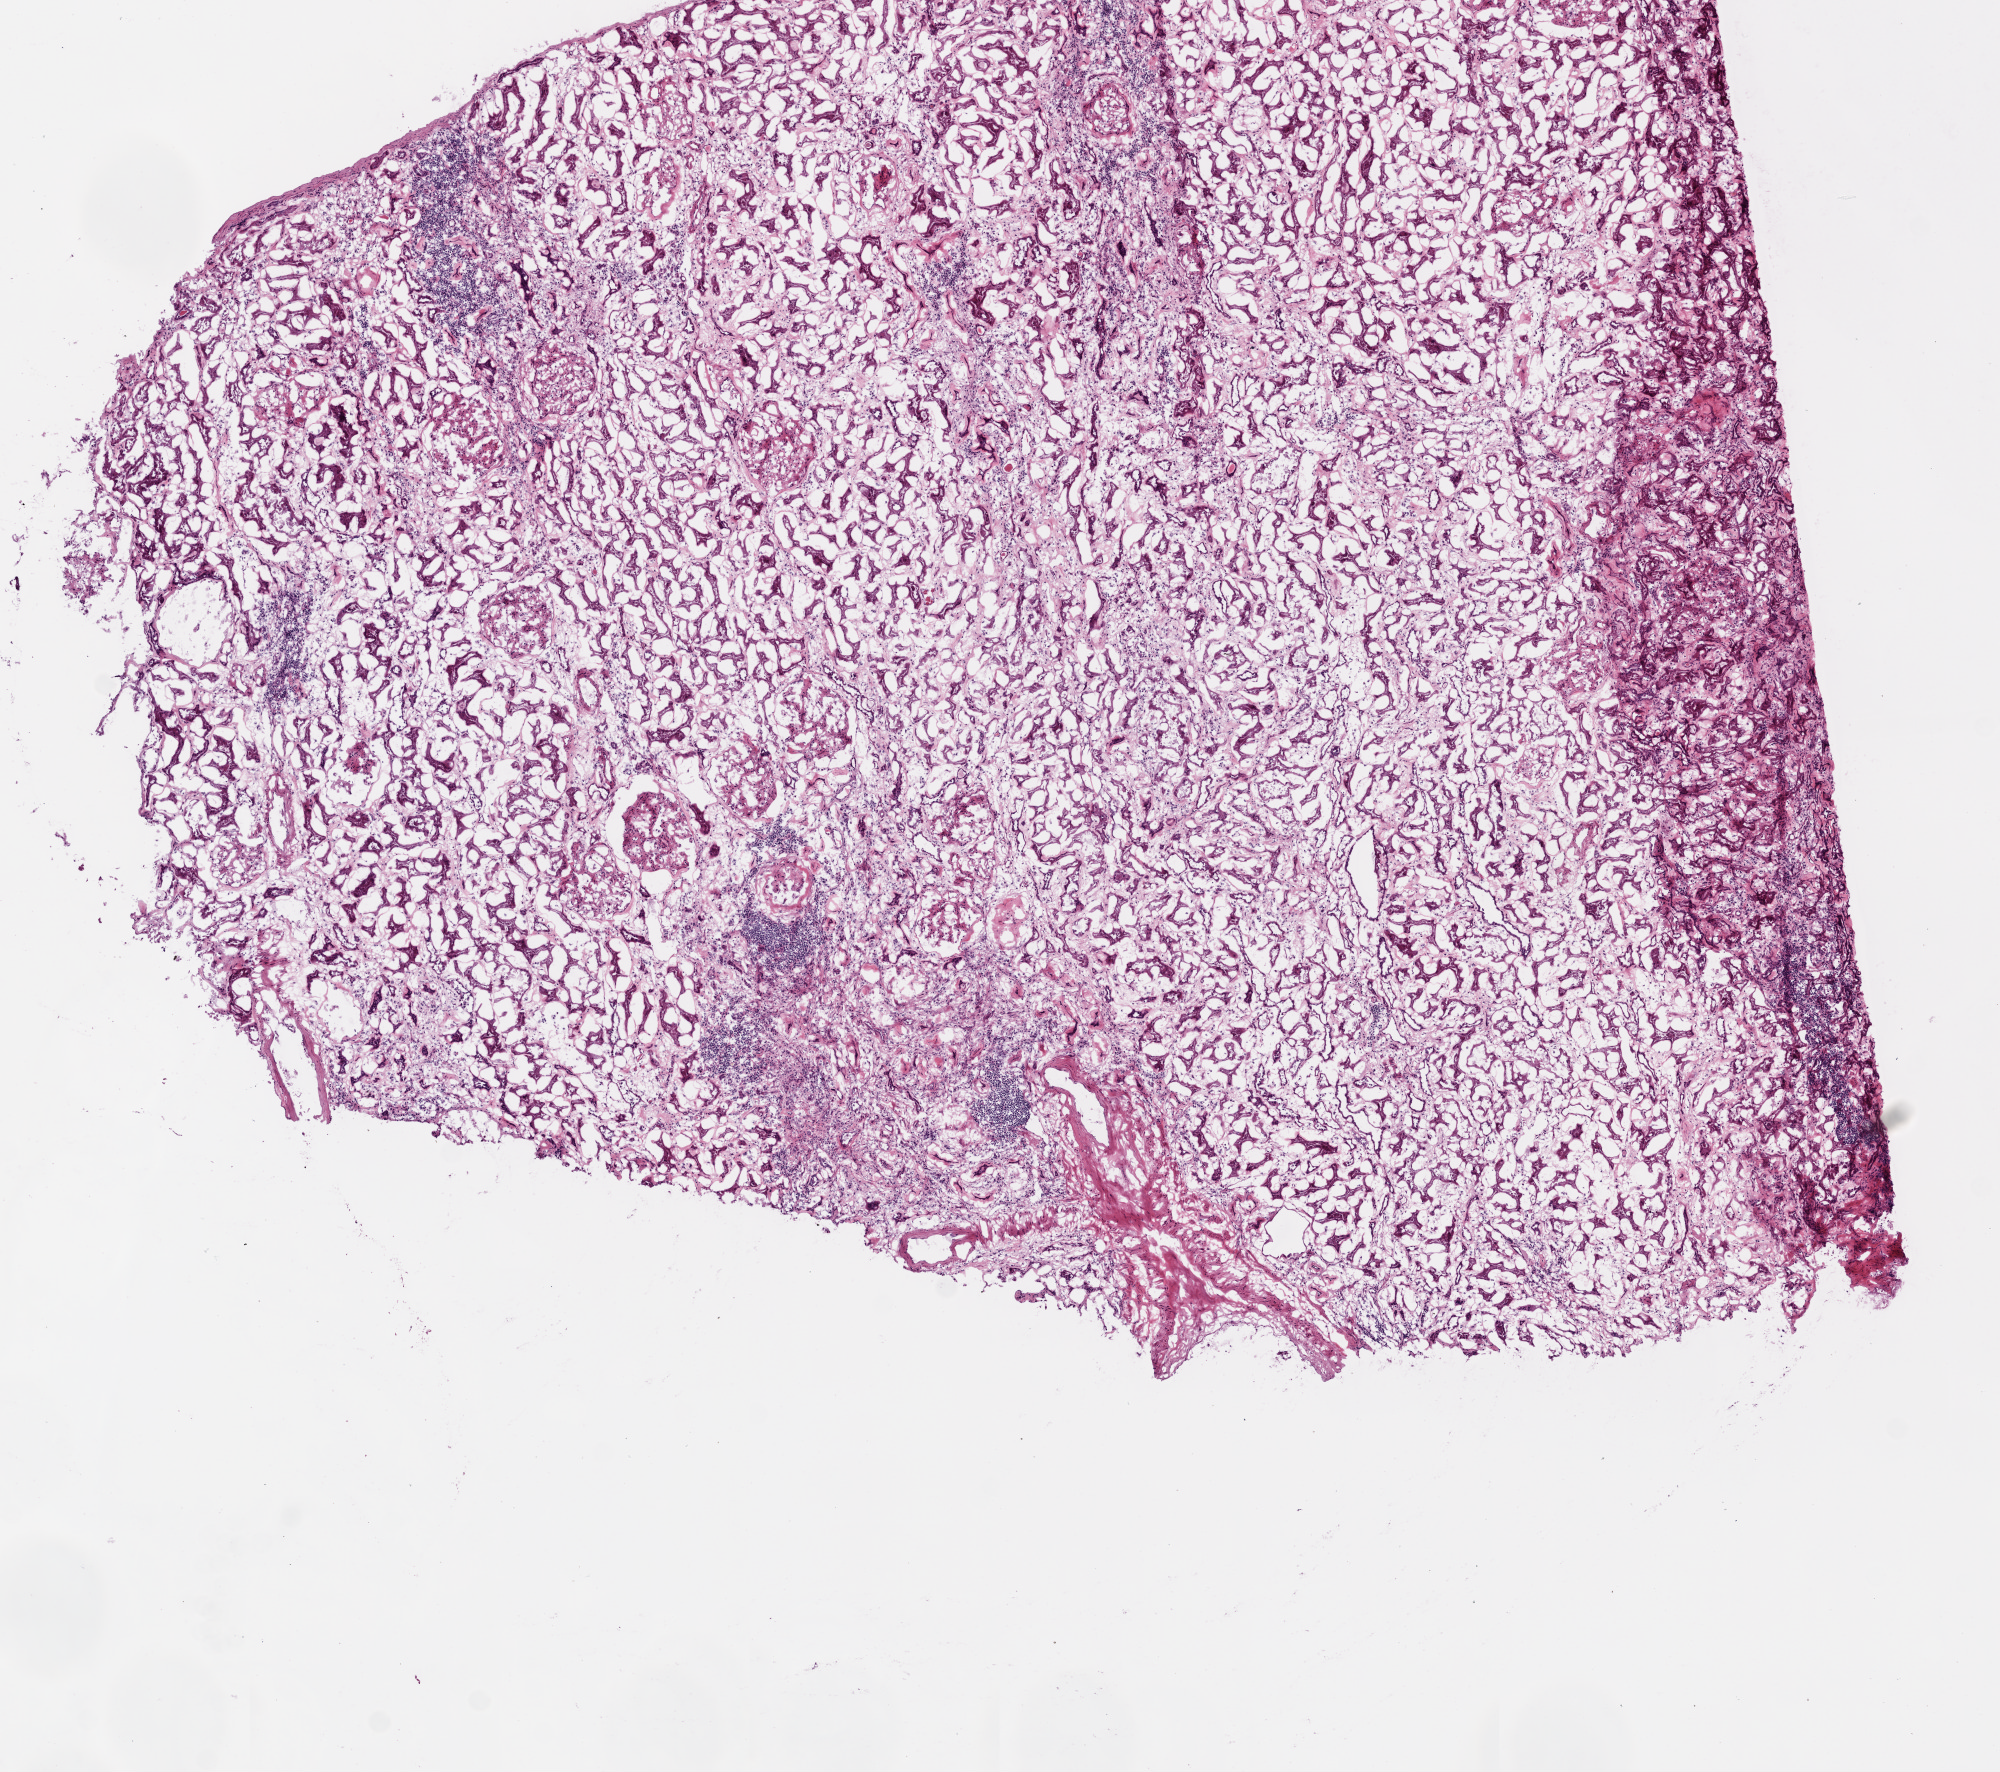
Digitized Hematoxylin and eosin (H&E) stained tissue section (whole slide) — low-resolution overview of the scanned area, about 8.0 x 7.1 mm (from a 20x scan); frozen section from the top of the tissue portion; kidney, solid tissue normal (non-tumour tissue) sample. Male patient; age at initial diagnosis 57 years.
This section: solid tissue normal sample (biorepository sample class). Patient diagnosis: Clear cell adenocarcinoma, NOS.